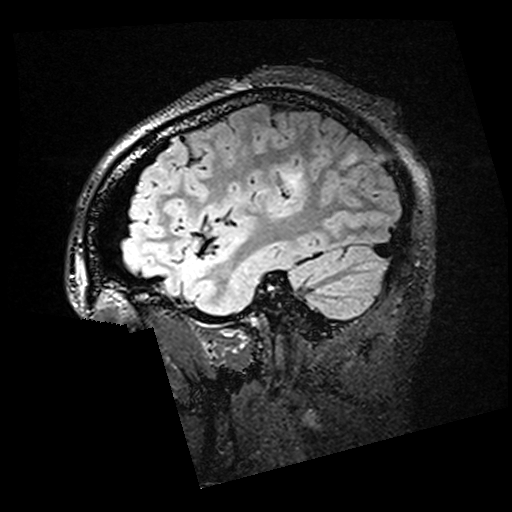
Brain MRI from a brain-tumour surgery series, one sagittal slice. Slice 45 of 176 in the series (ordered by position). T2 FLAIR. 1 mm slice thickness. 512 × 512 image matrix. Case-level facts recorded for this patient, not image findings: histopathology: Oligodendroglioma; WHO grade: 2; IDH mutation: yes; tumour location: Left Posterior Temporal.
Structures marked on this image (outlined manually by an expert reader):
- residual tumour: box from (x=281, y=173) to (x=305, y=191) px